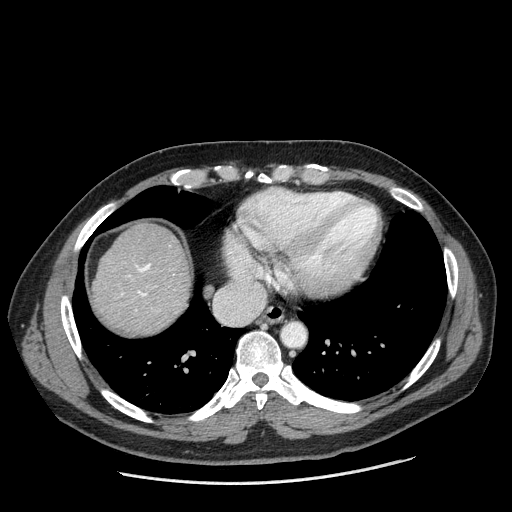
Contrast-enhanced abdominal CT (liver protocol), one axial slice; slice 173 of 198 in the series (ordered by position); reconstruction kernel STANDARD; one of 2 acquisitions stored at this slice position; soft-tissue window (W 400 / L 40 HU); 2.5 mm slice thickness; 512 × 512 image matrix. Case-level facts recorded for this patient, not image findings: diagnosis: hepatocellular carcinoma (patient treated with transarterial chemoembolisation; whether this scan precedes or follows treatment is not stated here); TNM stage (as recorded): Stage-II; Child-Pugh class: A; tumour differentiation: moderately differentiated; tumour size: 2.6 cm.
Outlined on this slice (semi-automatic segmentation, software-assisted and operator-edited):
- abdominal aorta: bounding box <282,323,305,346> (left, top, right, bottom; pixels)
- liver parenchyma outside the tumour (the mass and vessels are separate outlines, so this box may not span the whole liver): <92,222,190,334>
- liver vessels: <122,264,151,297>